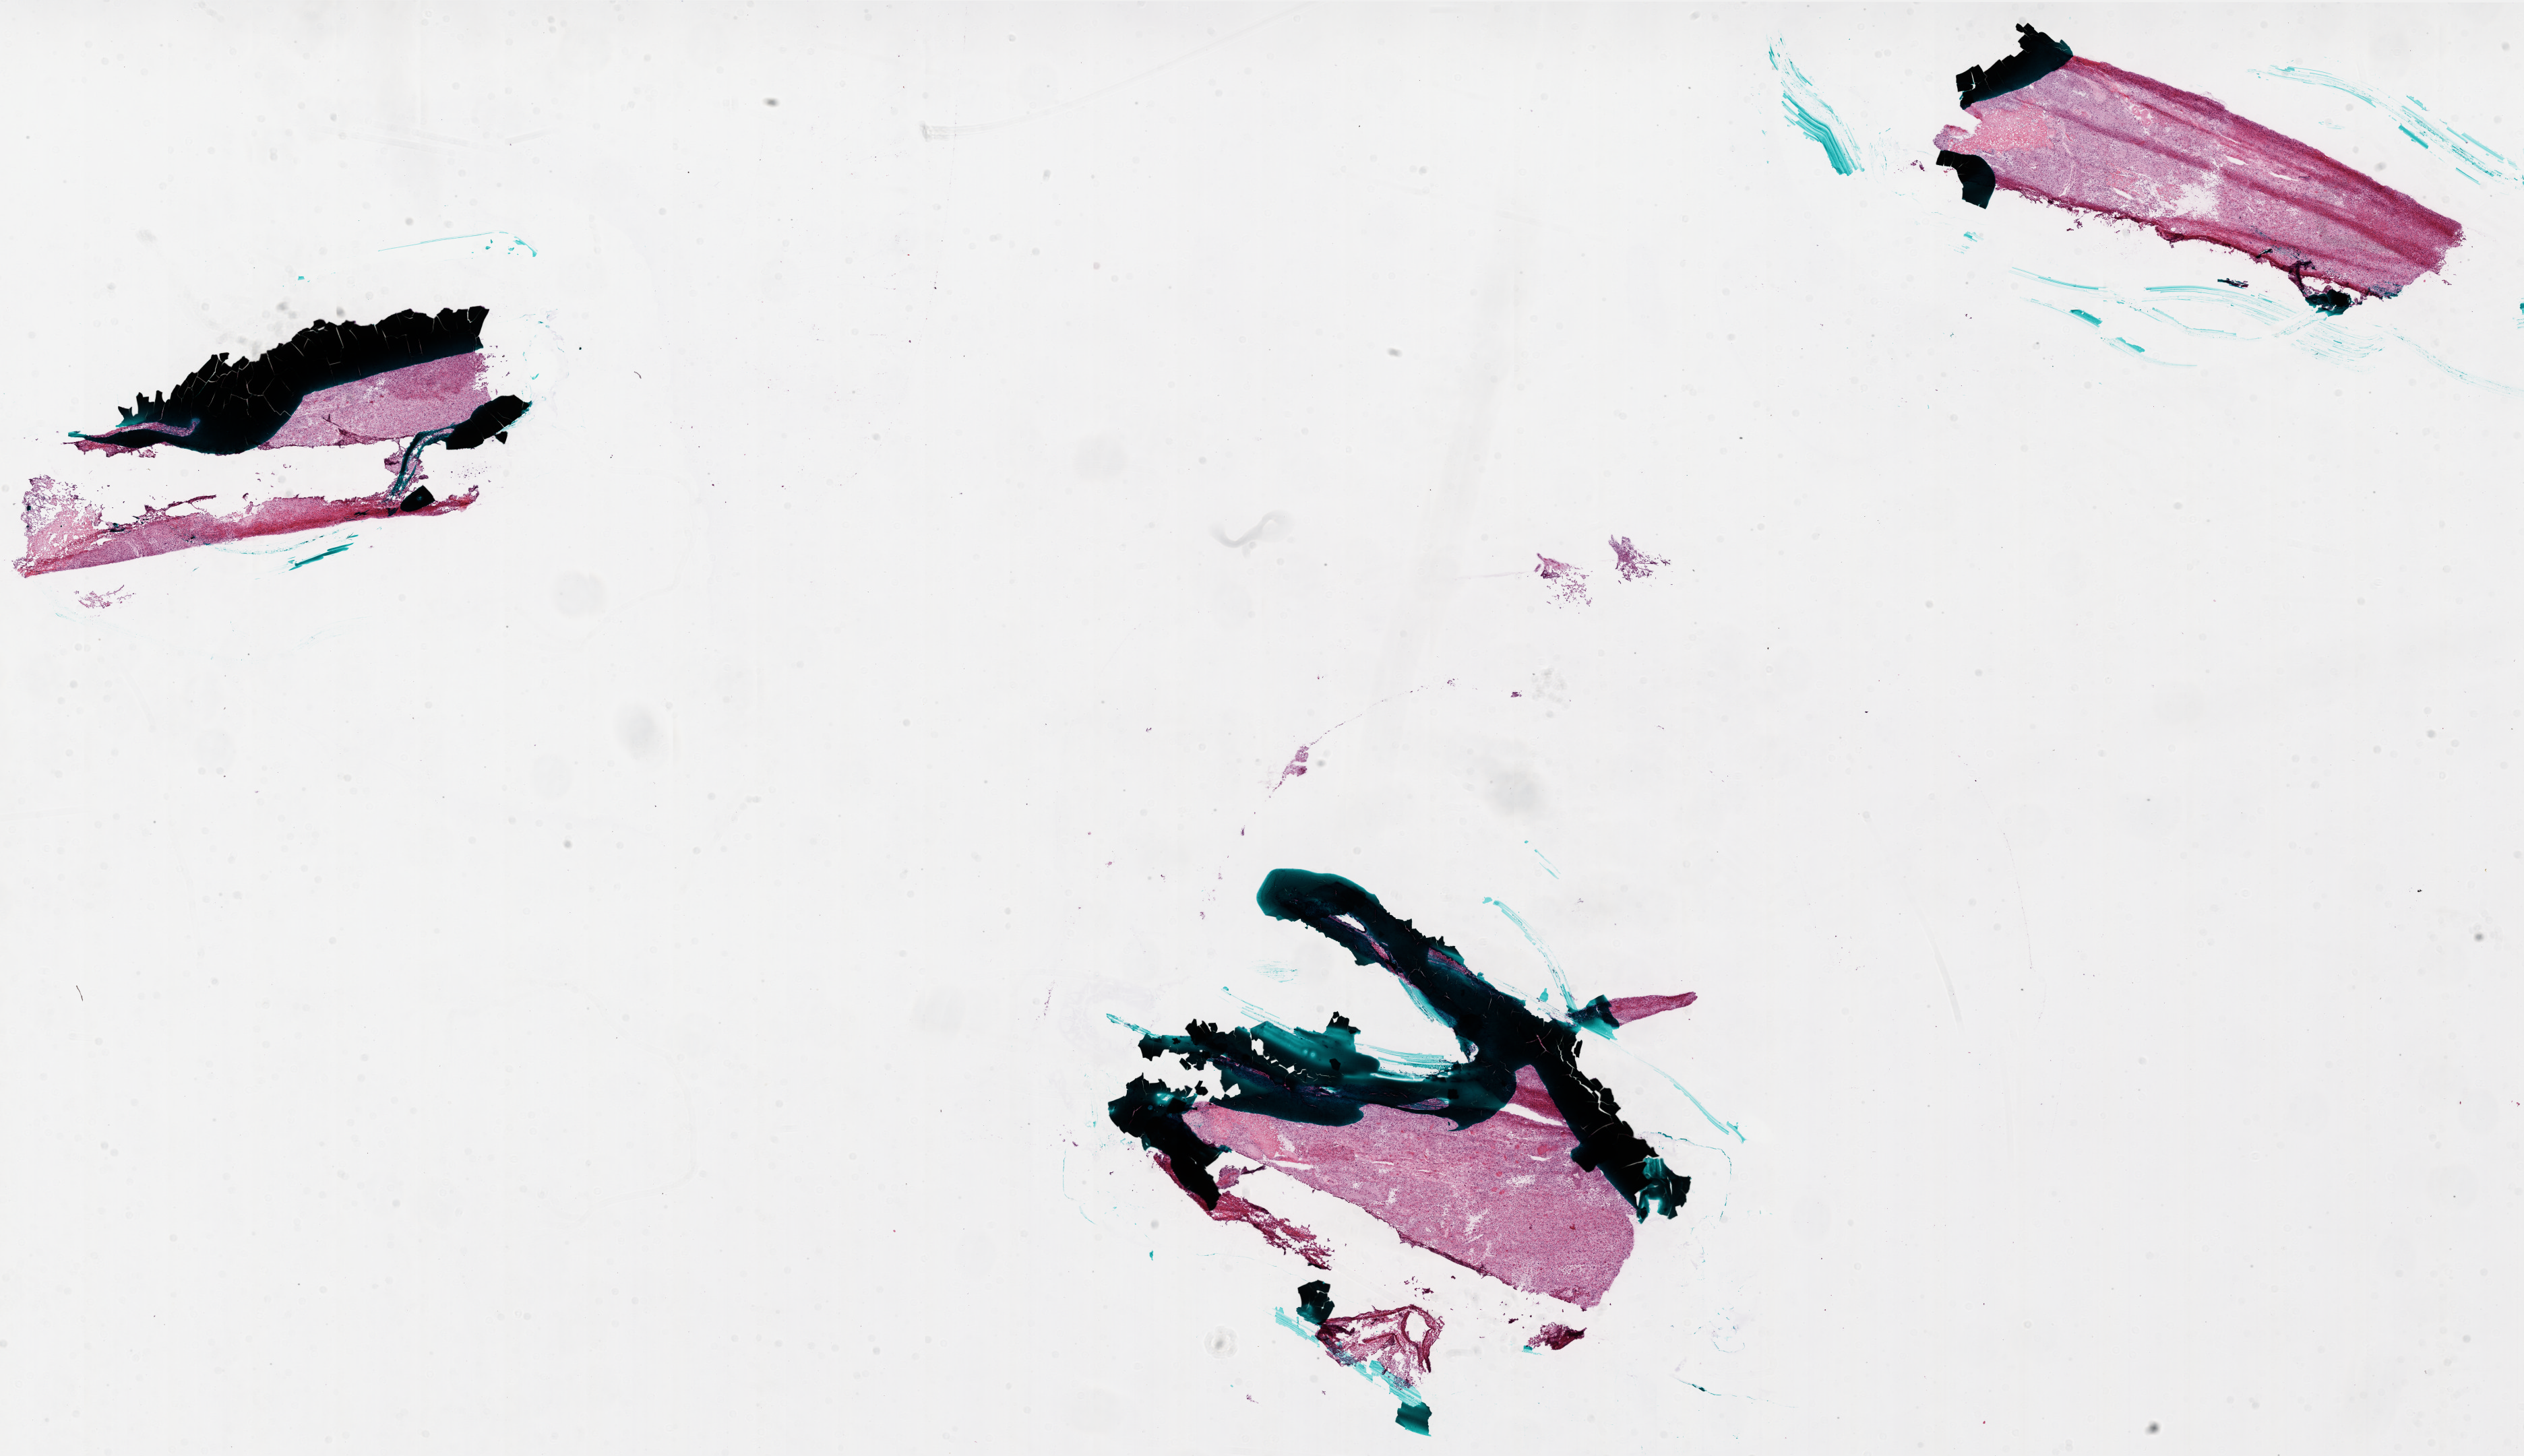
Digitized Hematoxylin and eosin (H&E) stained tissue section (whole slide) — low-resolution overview of the scanned area, about 30.0 x 17.3 mm (acquisition: 20x scan). Frozen section from the bottom of the tissue portion. Primary tumour sample from the brain. Female patient; age at initial diagnosis 74 years. Slide review estimates, as recorded: tumour cells 90%, tumour nuclei 100%.
Diagnosis: Glioblastoma.